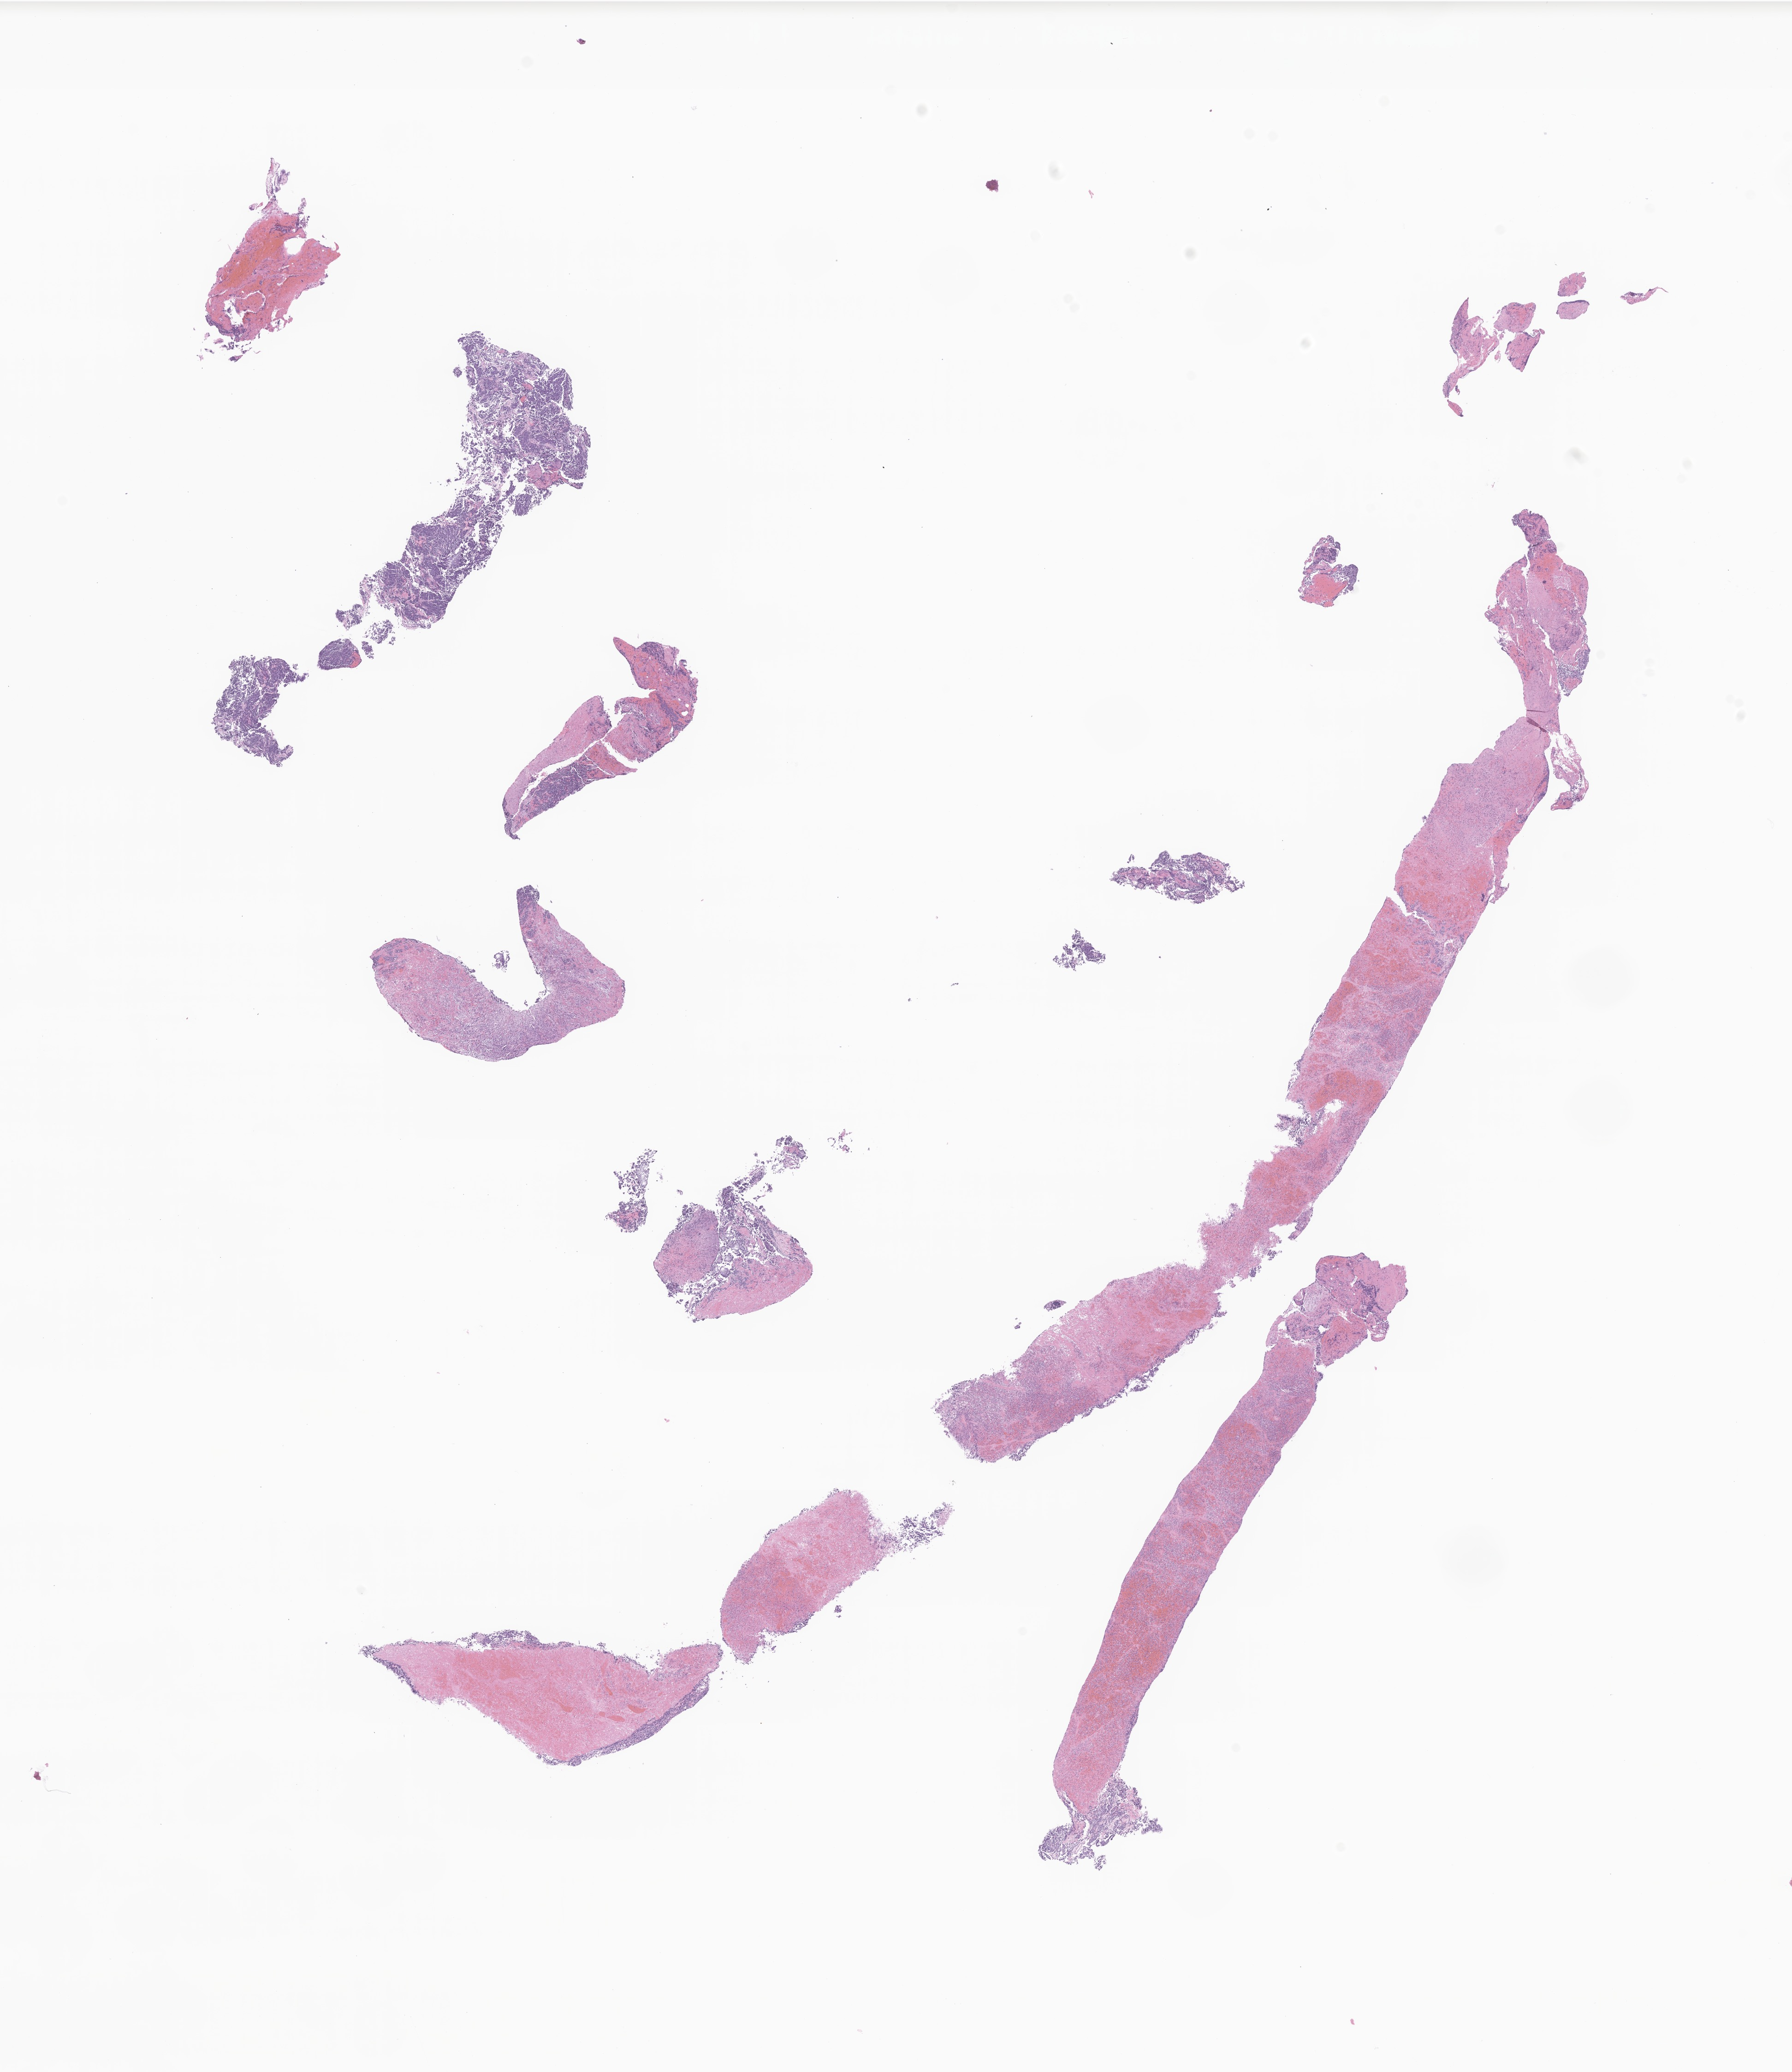
Whole-slide image, hematoxylin and eosin (H&E) stain of tumor tissue from the abdomen, whole scanned area (about 16.4 x 18.9 mm) shown as a low-resolution overview, FFPE section. Patient: male, age 45 months (3 years 9 months).
Diagnosis: Neuroblastoma, NOS.